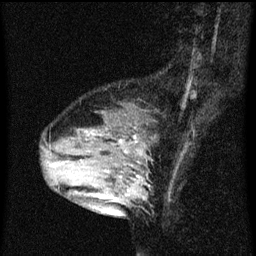
Breast MRI (dynamic contrast-enhanced), one sagittal slice. Position 19 of 60 along the scan axis. Dynamic contrast-enhanced series, image 2 of 3 at this slice position (ordered by acquisition). 1.5 T. TE 4.2 ms, TR 8 ms. 2 mm slice thickness. 256 × 256 image matrix, field of view 180 × 180 mm. Patient: female, 33 years.
Structures marked on this image (semi-automatically segmented with operator editing):
- analysis volume of interest (the breast-tissue region the enhancement analysis was run in; not a lesion): bounding box <61,126,148,213> (left, top, right, bottom; pixels)
- tumour enhancement mask (voxels above the 70 % enhancement threshold inside the analysis volume of interest): <119,136,140,197>